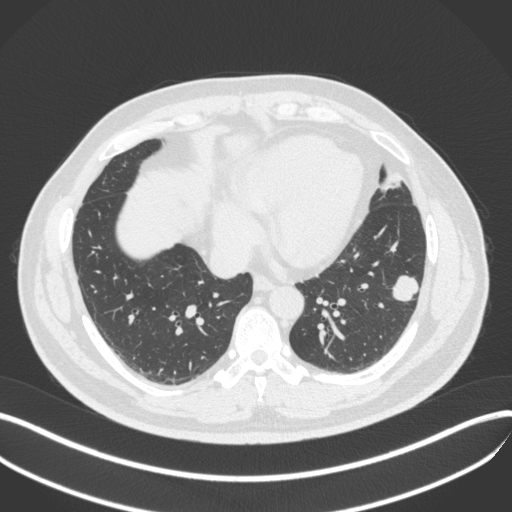
Chest CT, one axial slice. Position 147 of 420 along the scan axis. Reconstruction kernel B31f. 120 kVp. Lung window (W 1500 / L -600 HU). 1 mm slice thickness. 512 × 512 image matrix, field of view 400 × 400 mm. Patient: male, 39 years. From the clinical record (not read from this slice): clinical TNM (as recorded): T2a N0 M0; histopathological grade: G2-3.
Outlined on this slice (bounding box drawn by a radiologist):
- lung tumour (recorded histology: adenocarcinoma): bounding box [x1, y1, x2, y2] px = [387, 268, 423, 306]